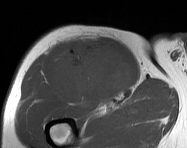
MRI of an extremity soft-tissue mass, one axial slice; slice 99 of 114 in the series (ordered by position); MR volume resampled by the dataset authors to the PET/CT grid (not the native acquisition matrix); 3.27 mm slice thickness; 187 × 148 image matrix, field of view 183 × 145 mm. Male patient. From the clinical record (not read from this slice): histological type: pleiomorphic leiomyosarcoma; grade: intermediate; site of the primary tumour: right thigh.
Outlined on this slice (expert contour drawn on MRI and transferred to this co-registered scan by the dataset authors):
- gross tumour volume including surrounding oedema: box from (x=52, y=38) to (x=133, y=107) px
- gross tumour volume (mass): (x=54, y=38)–(x=133, y=107)